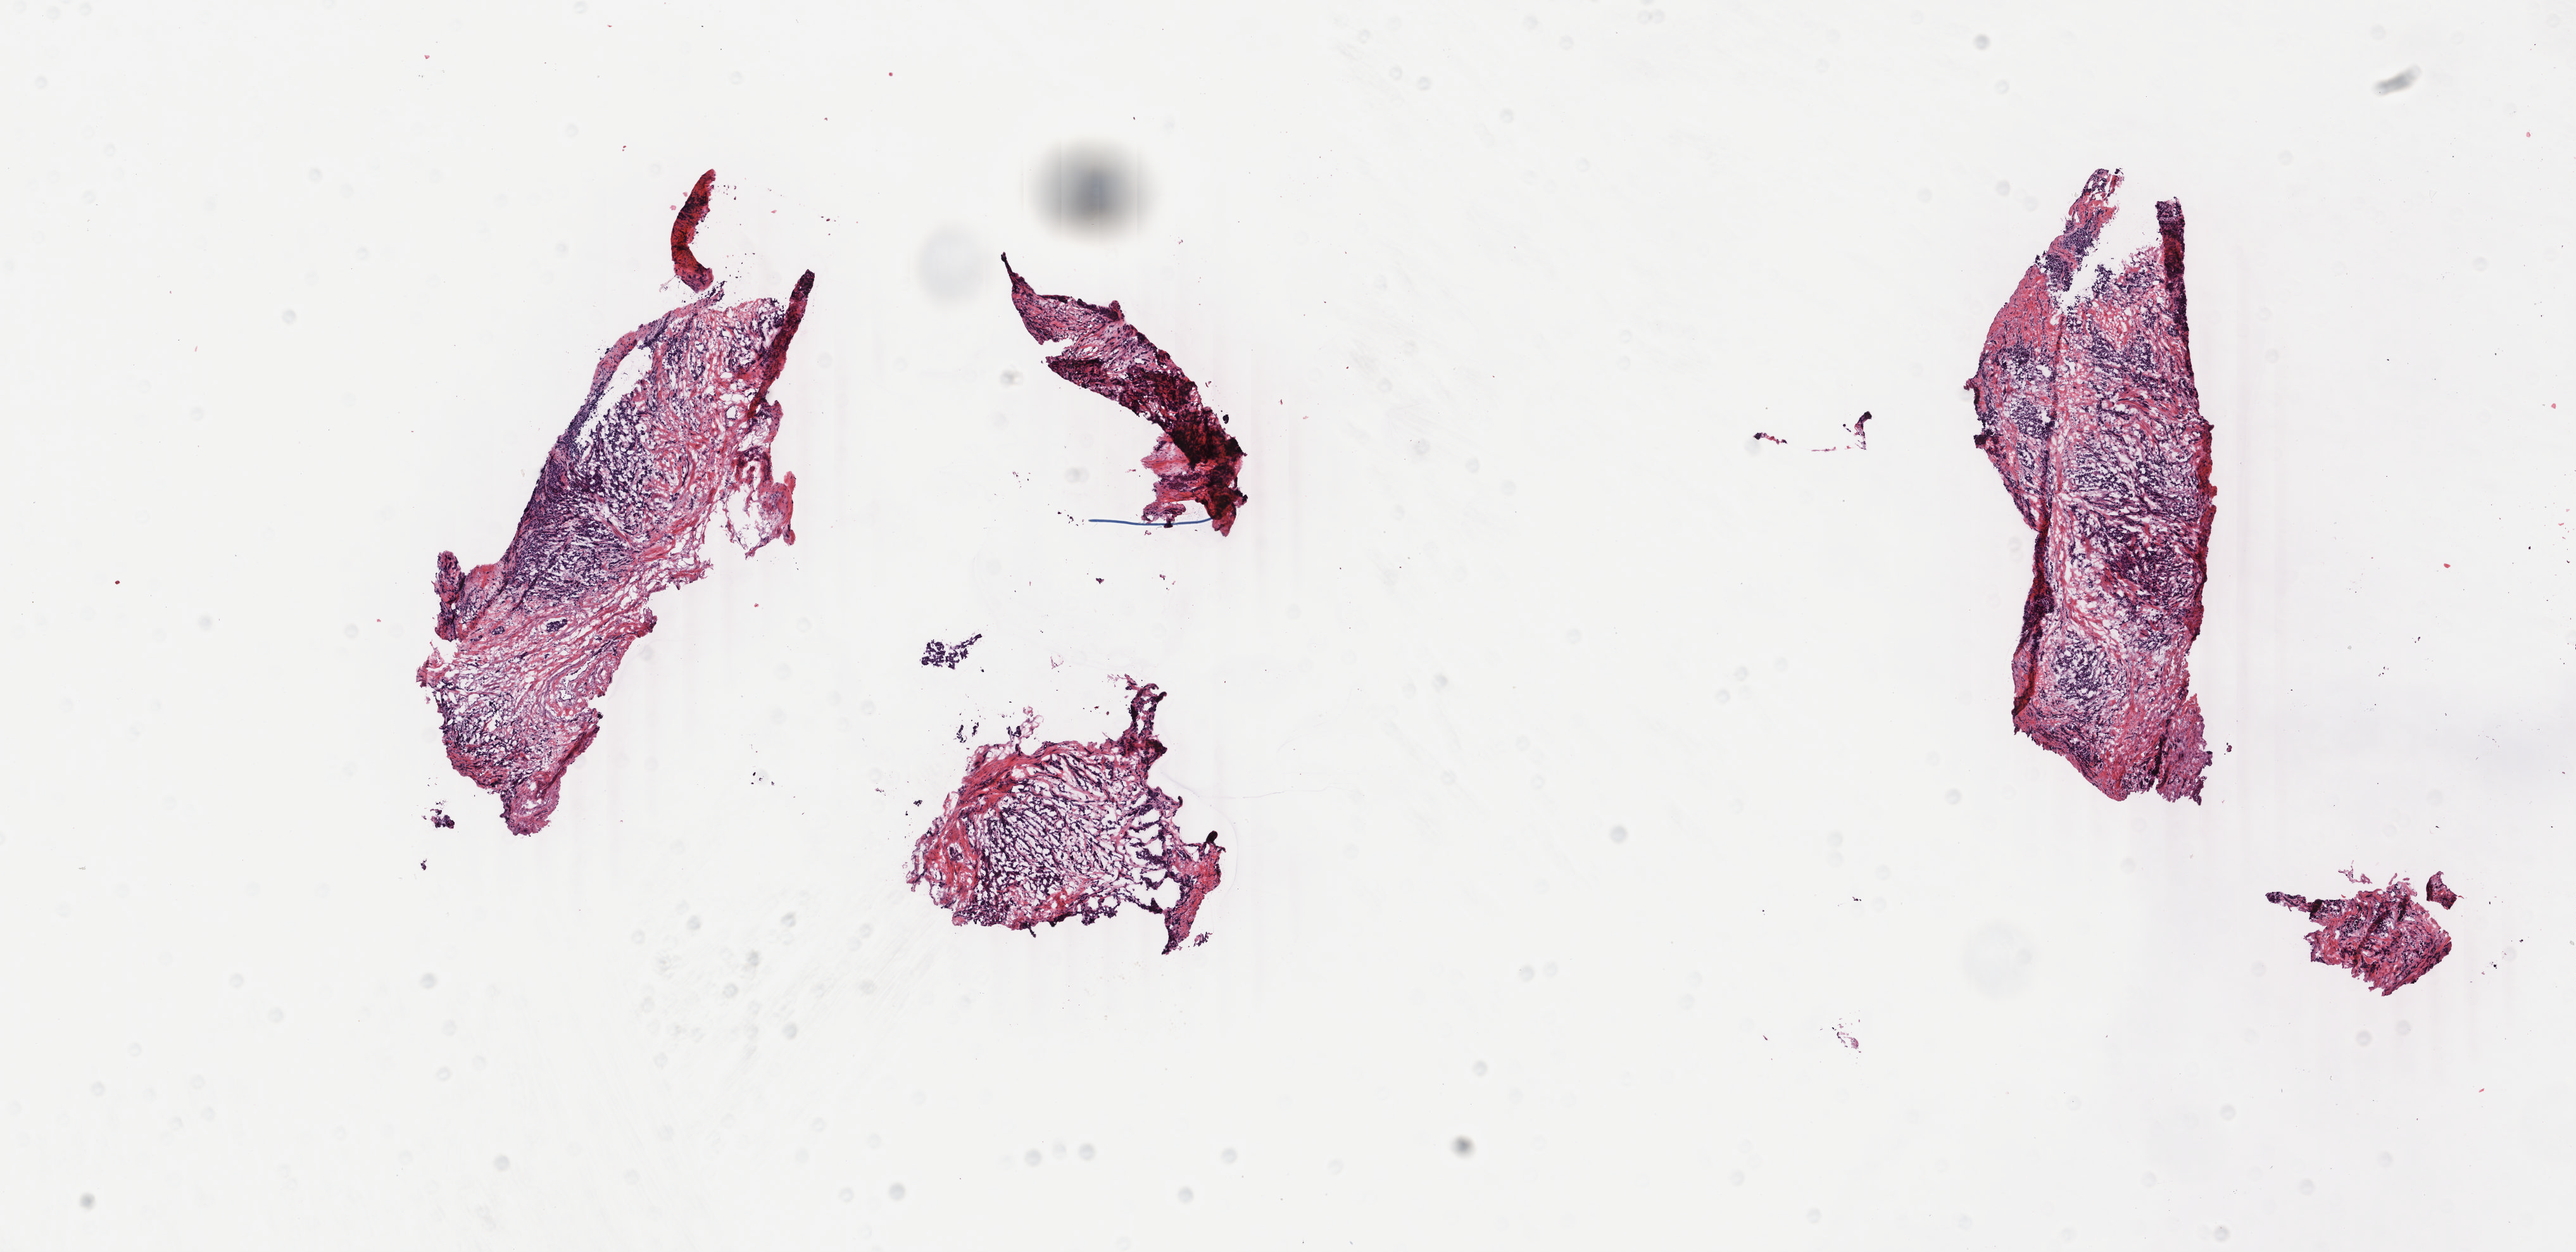
Whole-slide histology image, H&E — whole scanned area (about 16.2 x 7.9 mm, slide scanned at 40x) shown as a low-resolution overview. Frozen section. Breast, primary tumour sample. Patient: female, age at initial diagnosis 71 years. Pathologist review of this section (percent, as recorded): tumour cells 79%, tumour nuclei 88%, normal cells 10%, stromal cells 10%, necrosis 1%. Inflammatory infiltration, as recorded: lymphocyte infiltration 4%, monocyte infiltration 0%, neutrophil infiltration 0%.
Histologic diagnosis: Infiltrating duct carcinoma, NOS. TNM: T2 N0 (i-) M0. AJCC pathologic stage: IIA.